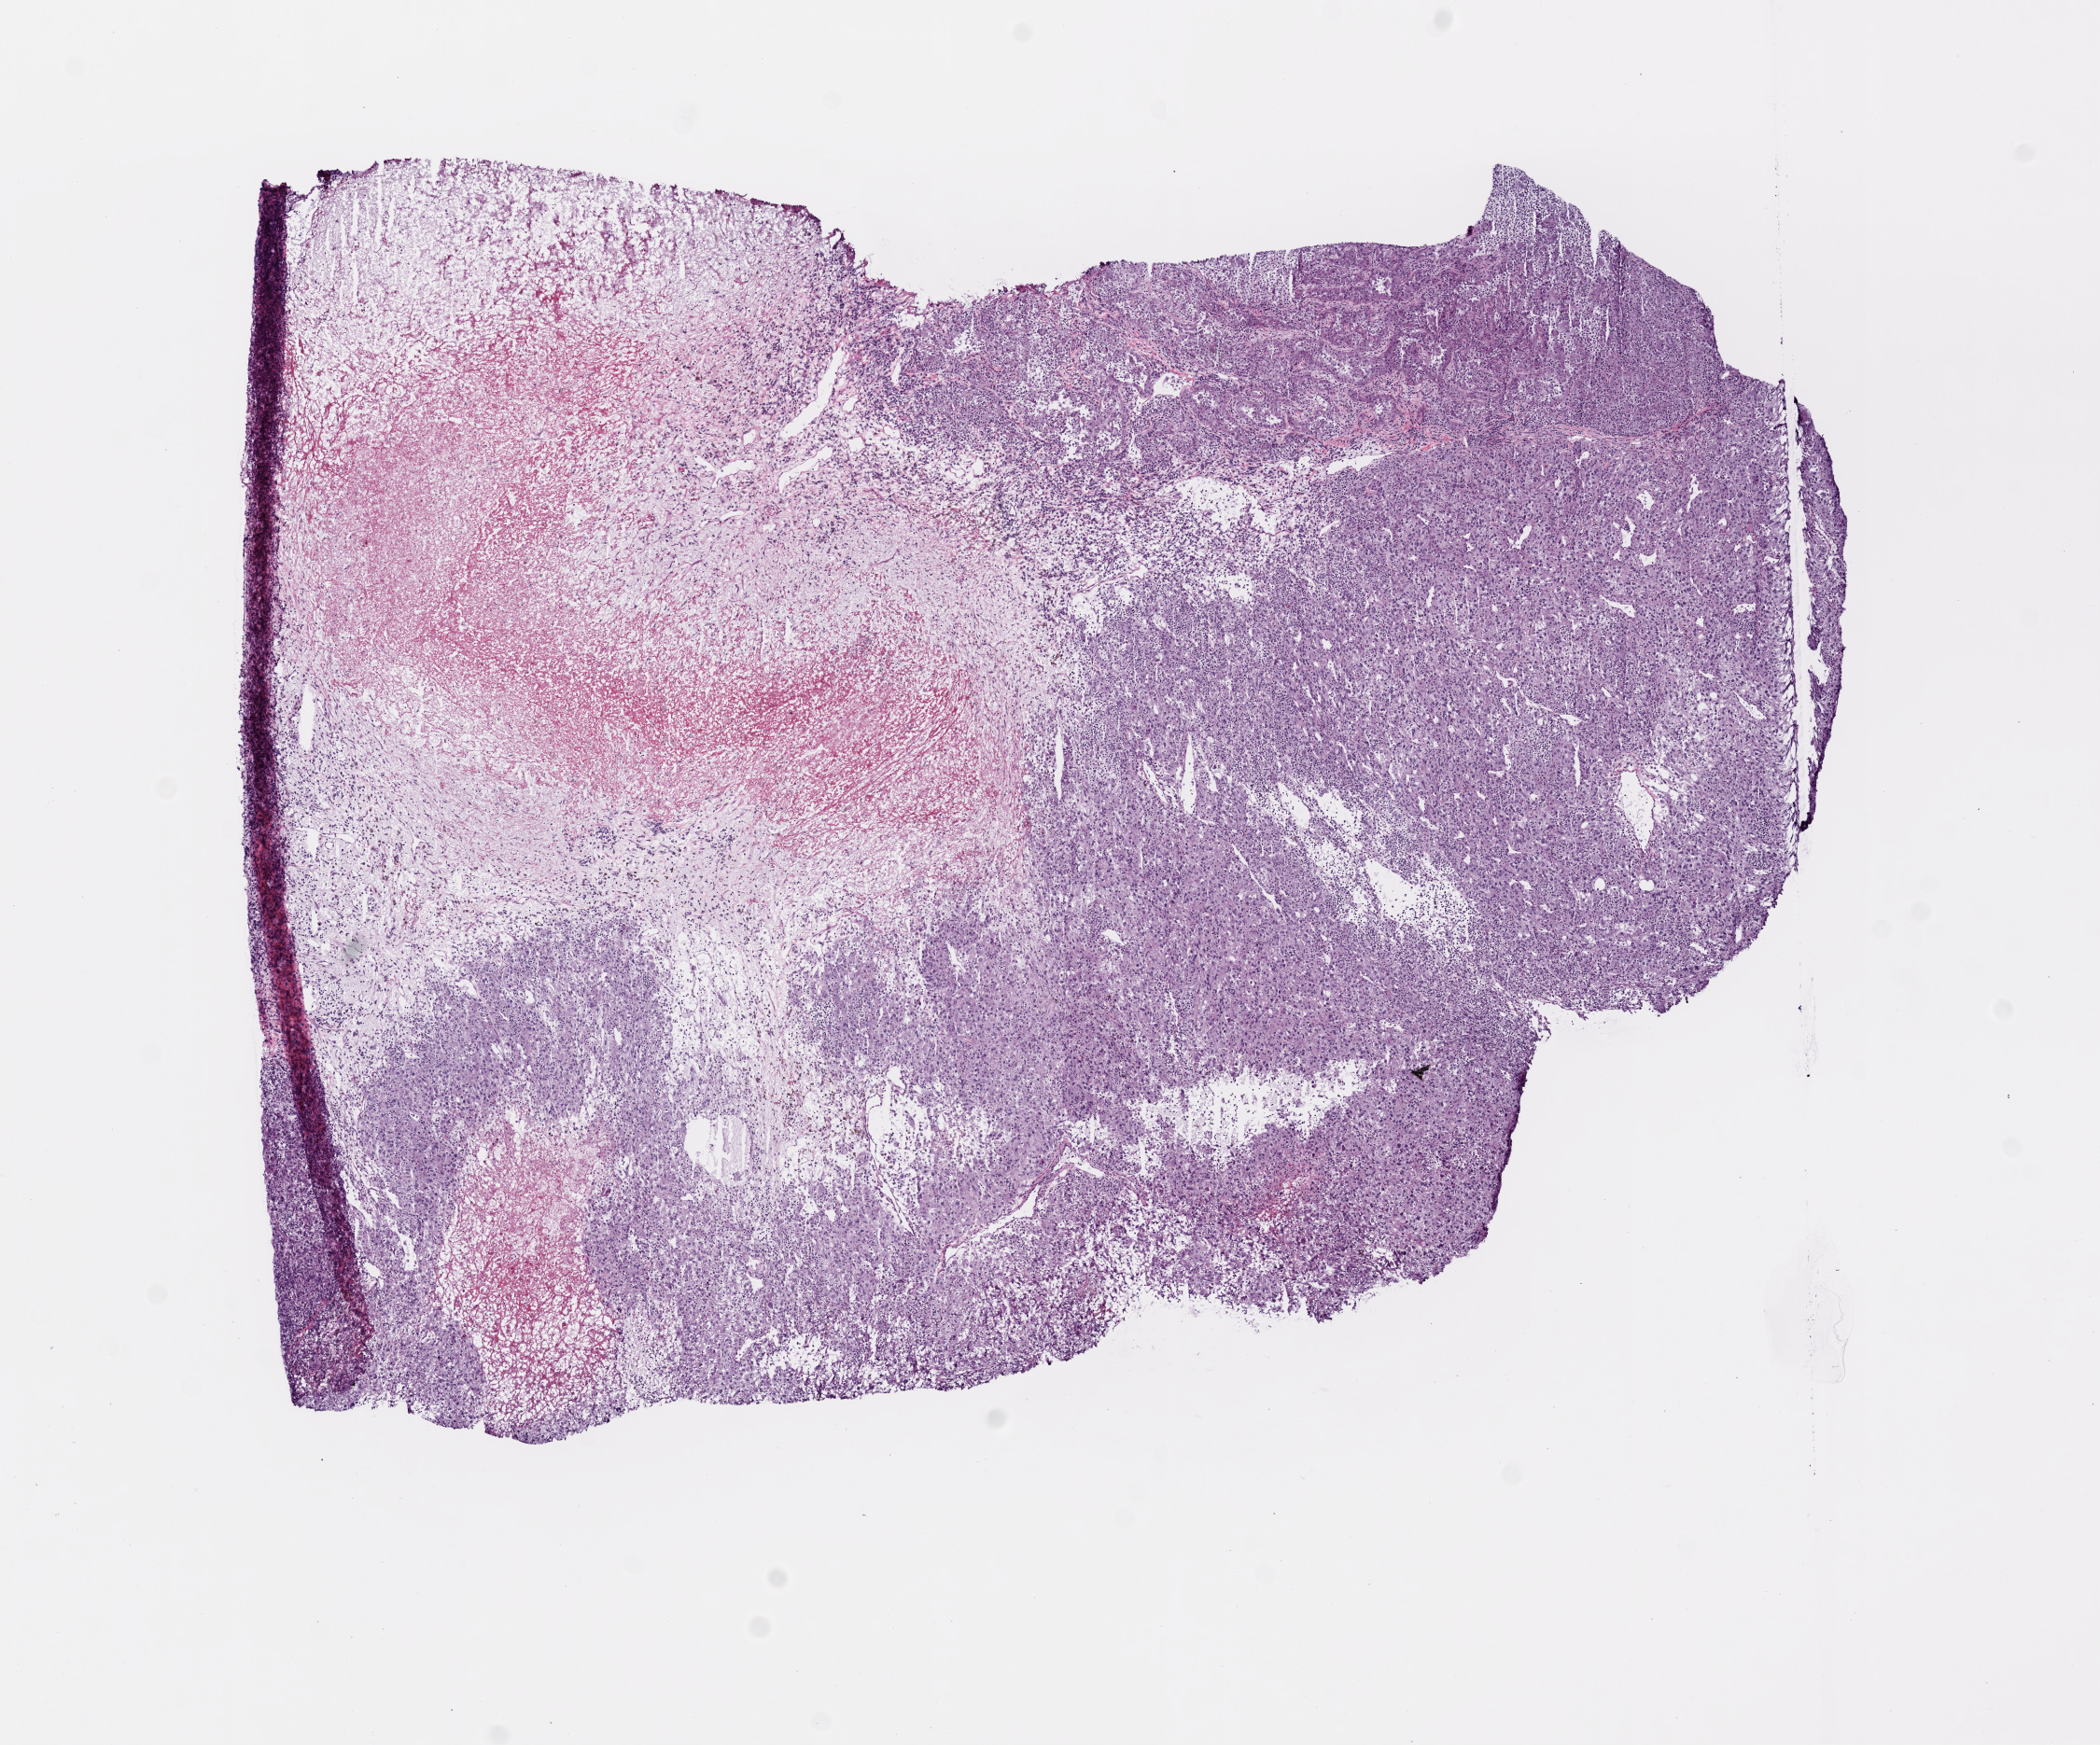
H&E-stained whole-slide image — a low-resolution overview of the entire scanned area, about 9.0 x 7.5 mm; frozen section from the top of the tissue portion; sample: primary tumour, kidney. Patient: female, age at initial diagnosis 65 years. Histologic grade: G3 (poorly differentiated). Slide review estimates, as recorded: tumour cells 62%, tumour nuclei 80%, normal cells 0%, stromal cells 20%, necrosis 18%.
AJCC pathologic stage: I. Pathologic diagnosis: Clear cell adenocarcinoma, NOS.